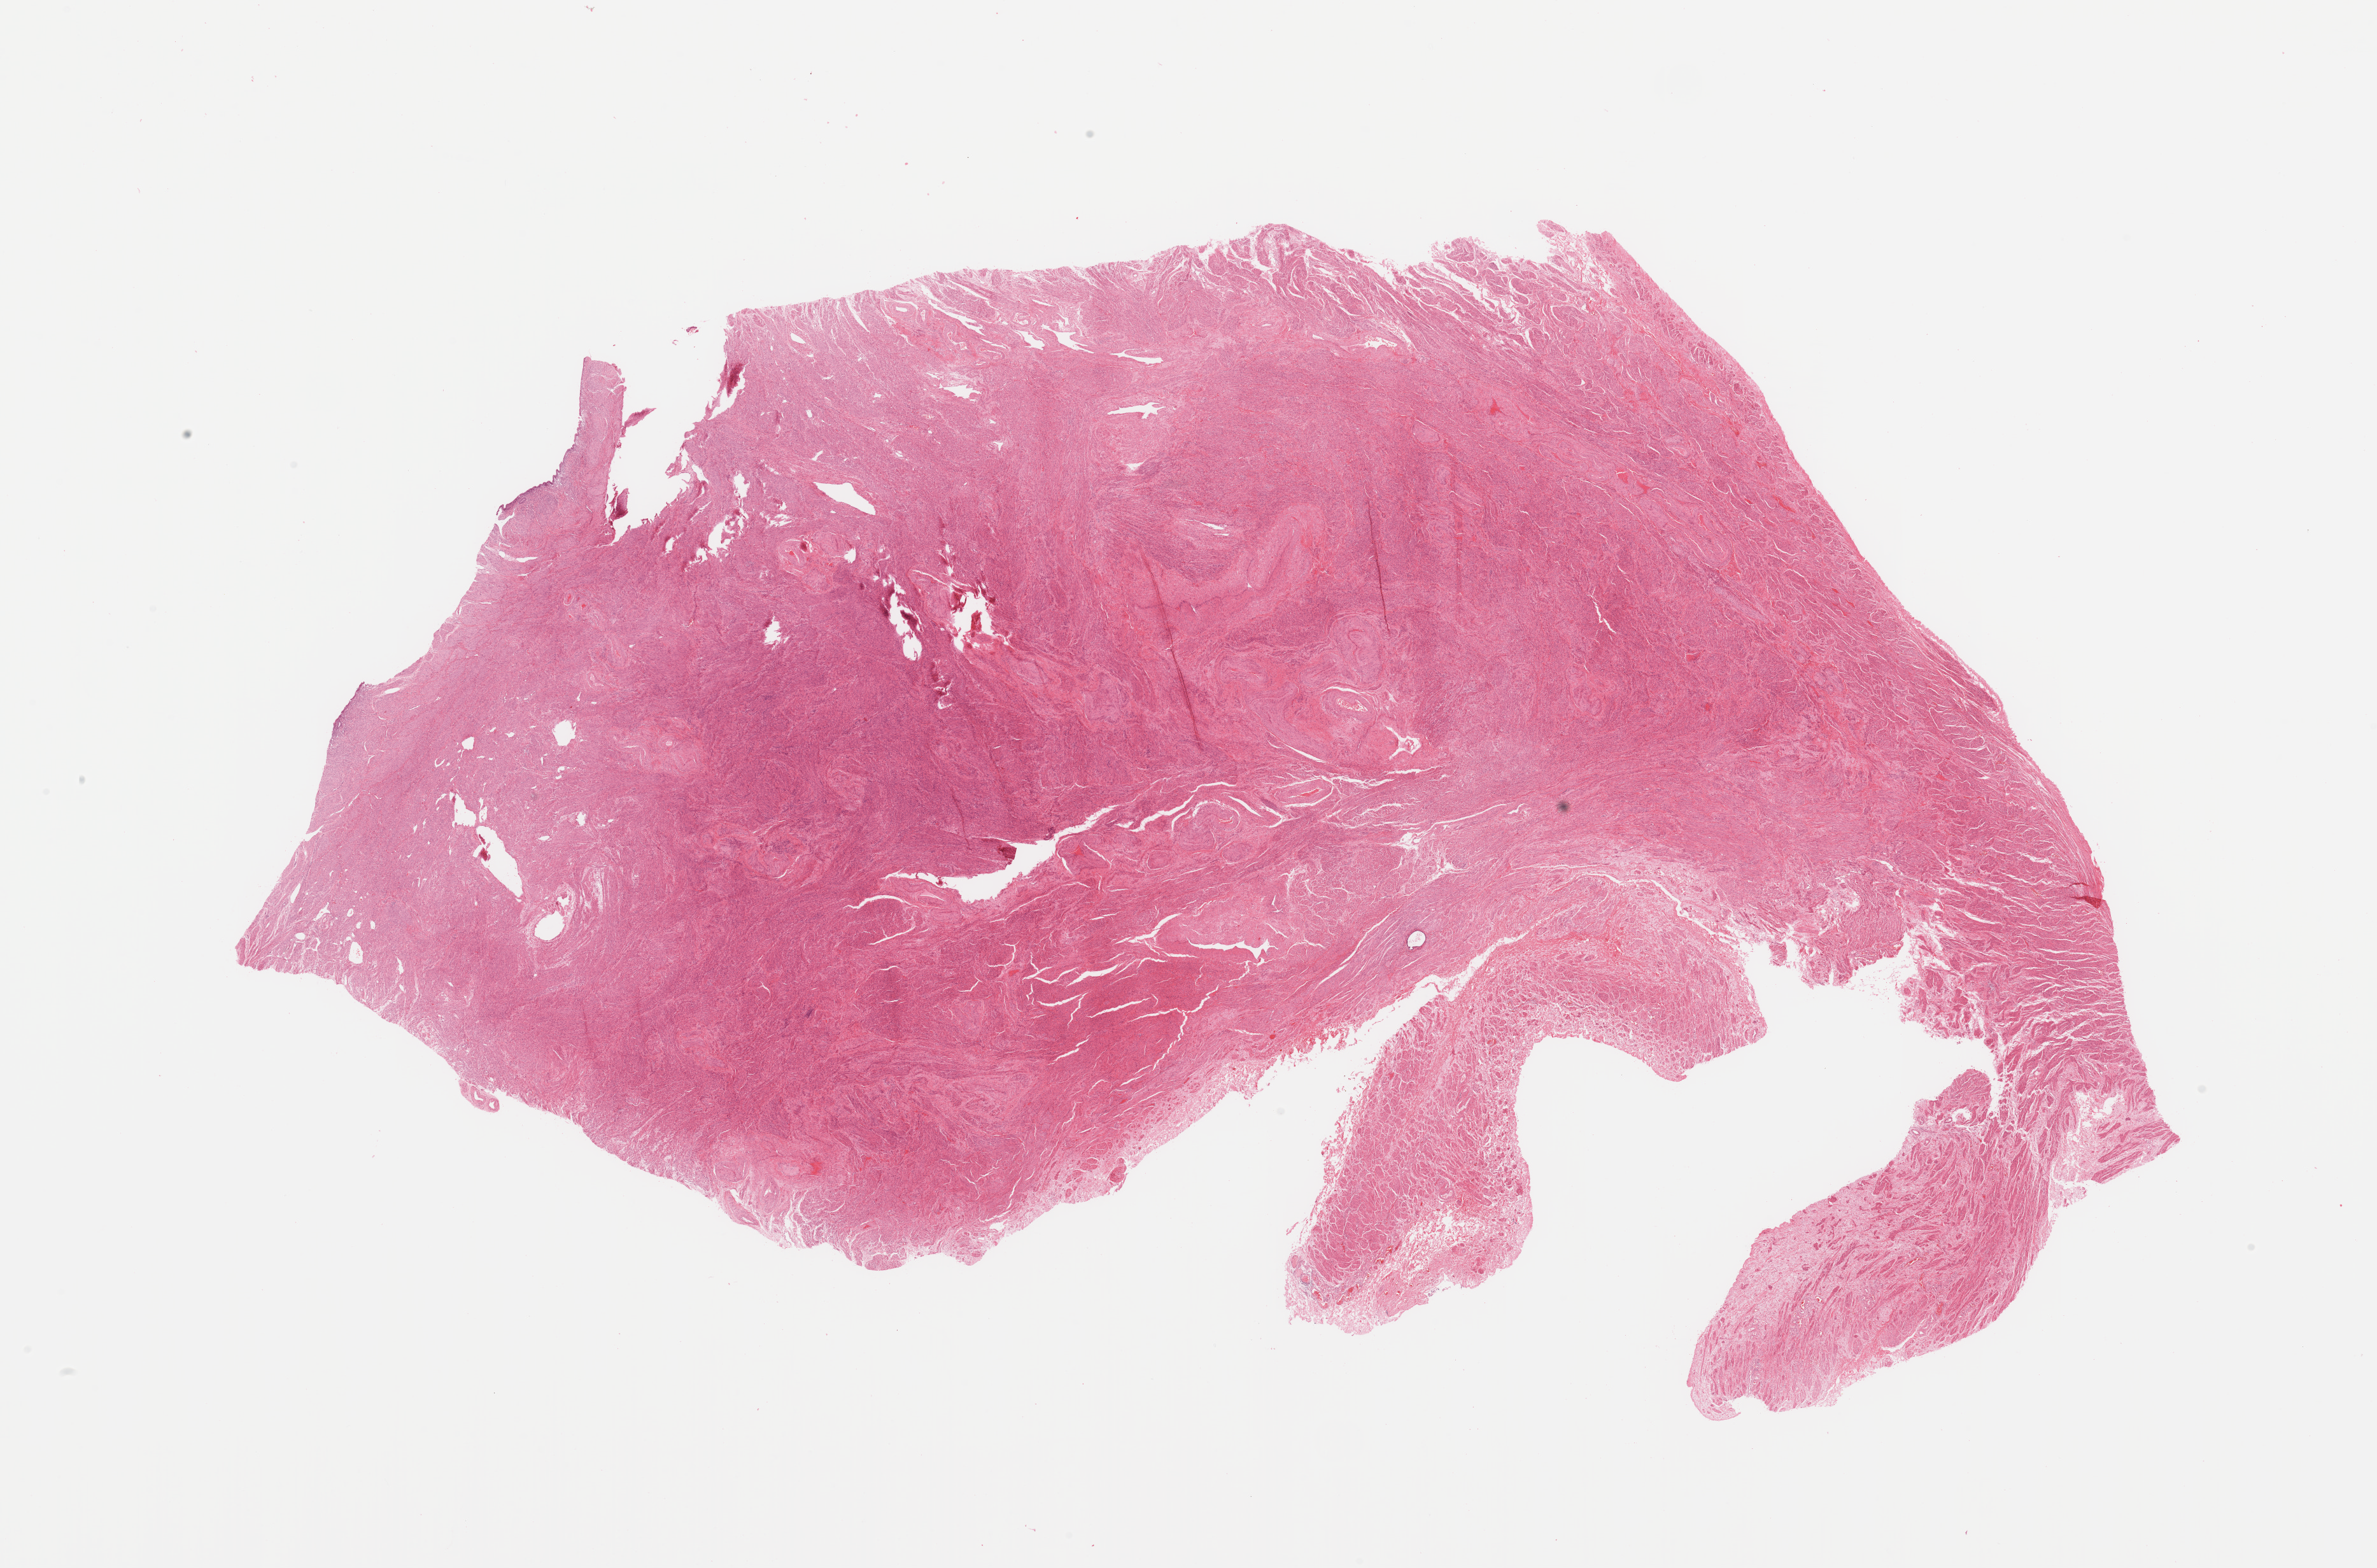
Whole-slide histology image, H&E-stained, a low-resolution overview of the entire scanned area, about 29.5 x 19.5 mm (slide scanned at 20x). Uterus, normal (non-tumour) tissue. Female, 77 y/o.
This section: normal (non-tumour) tissue from the same patient. Patient diagnosis: Endometrioid adenocarcinoma, NOS.